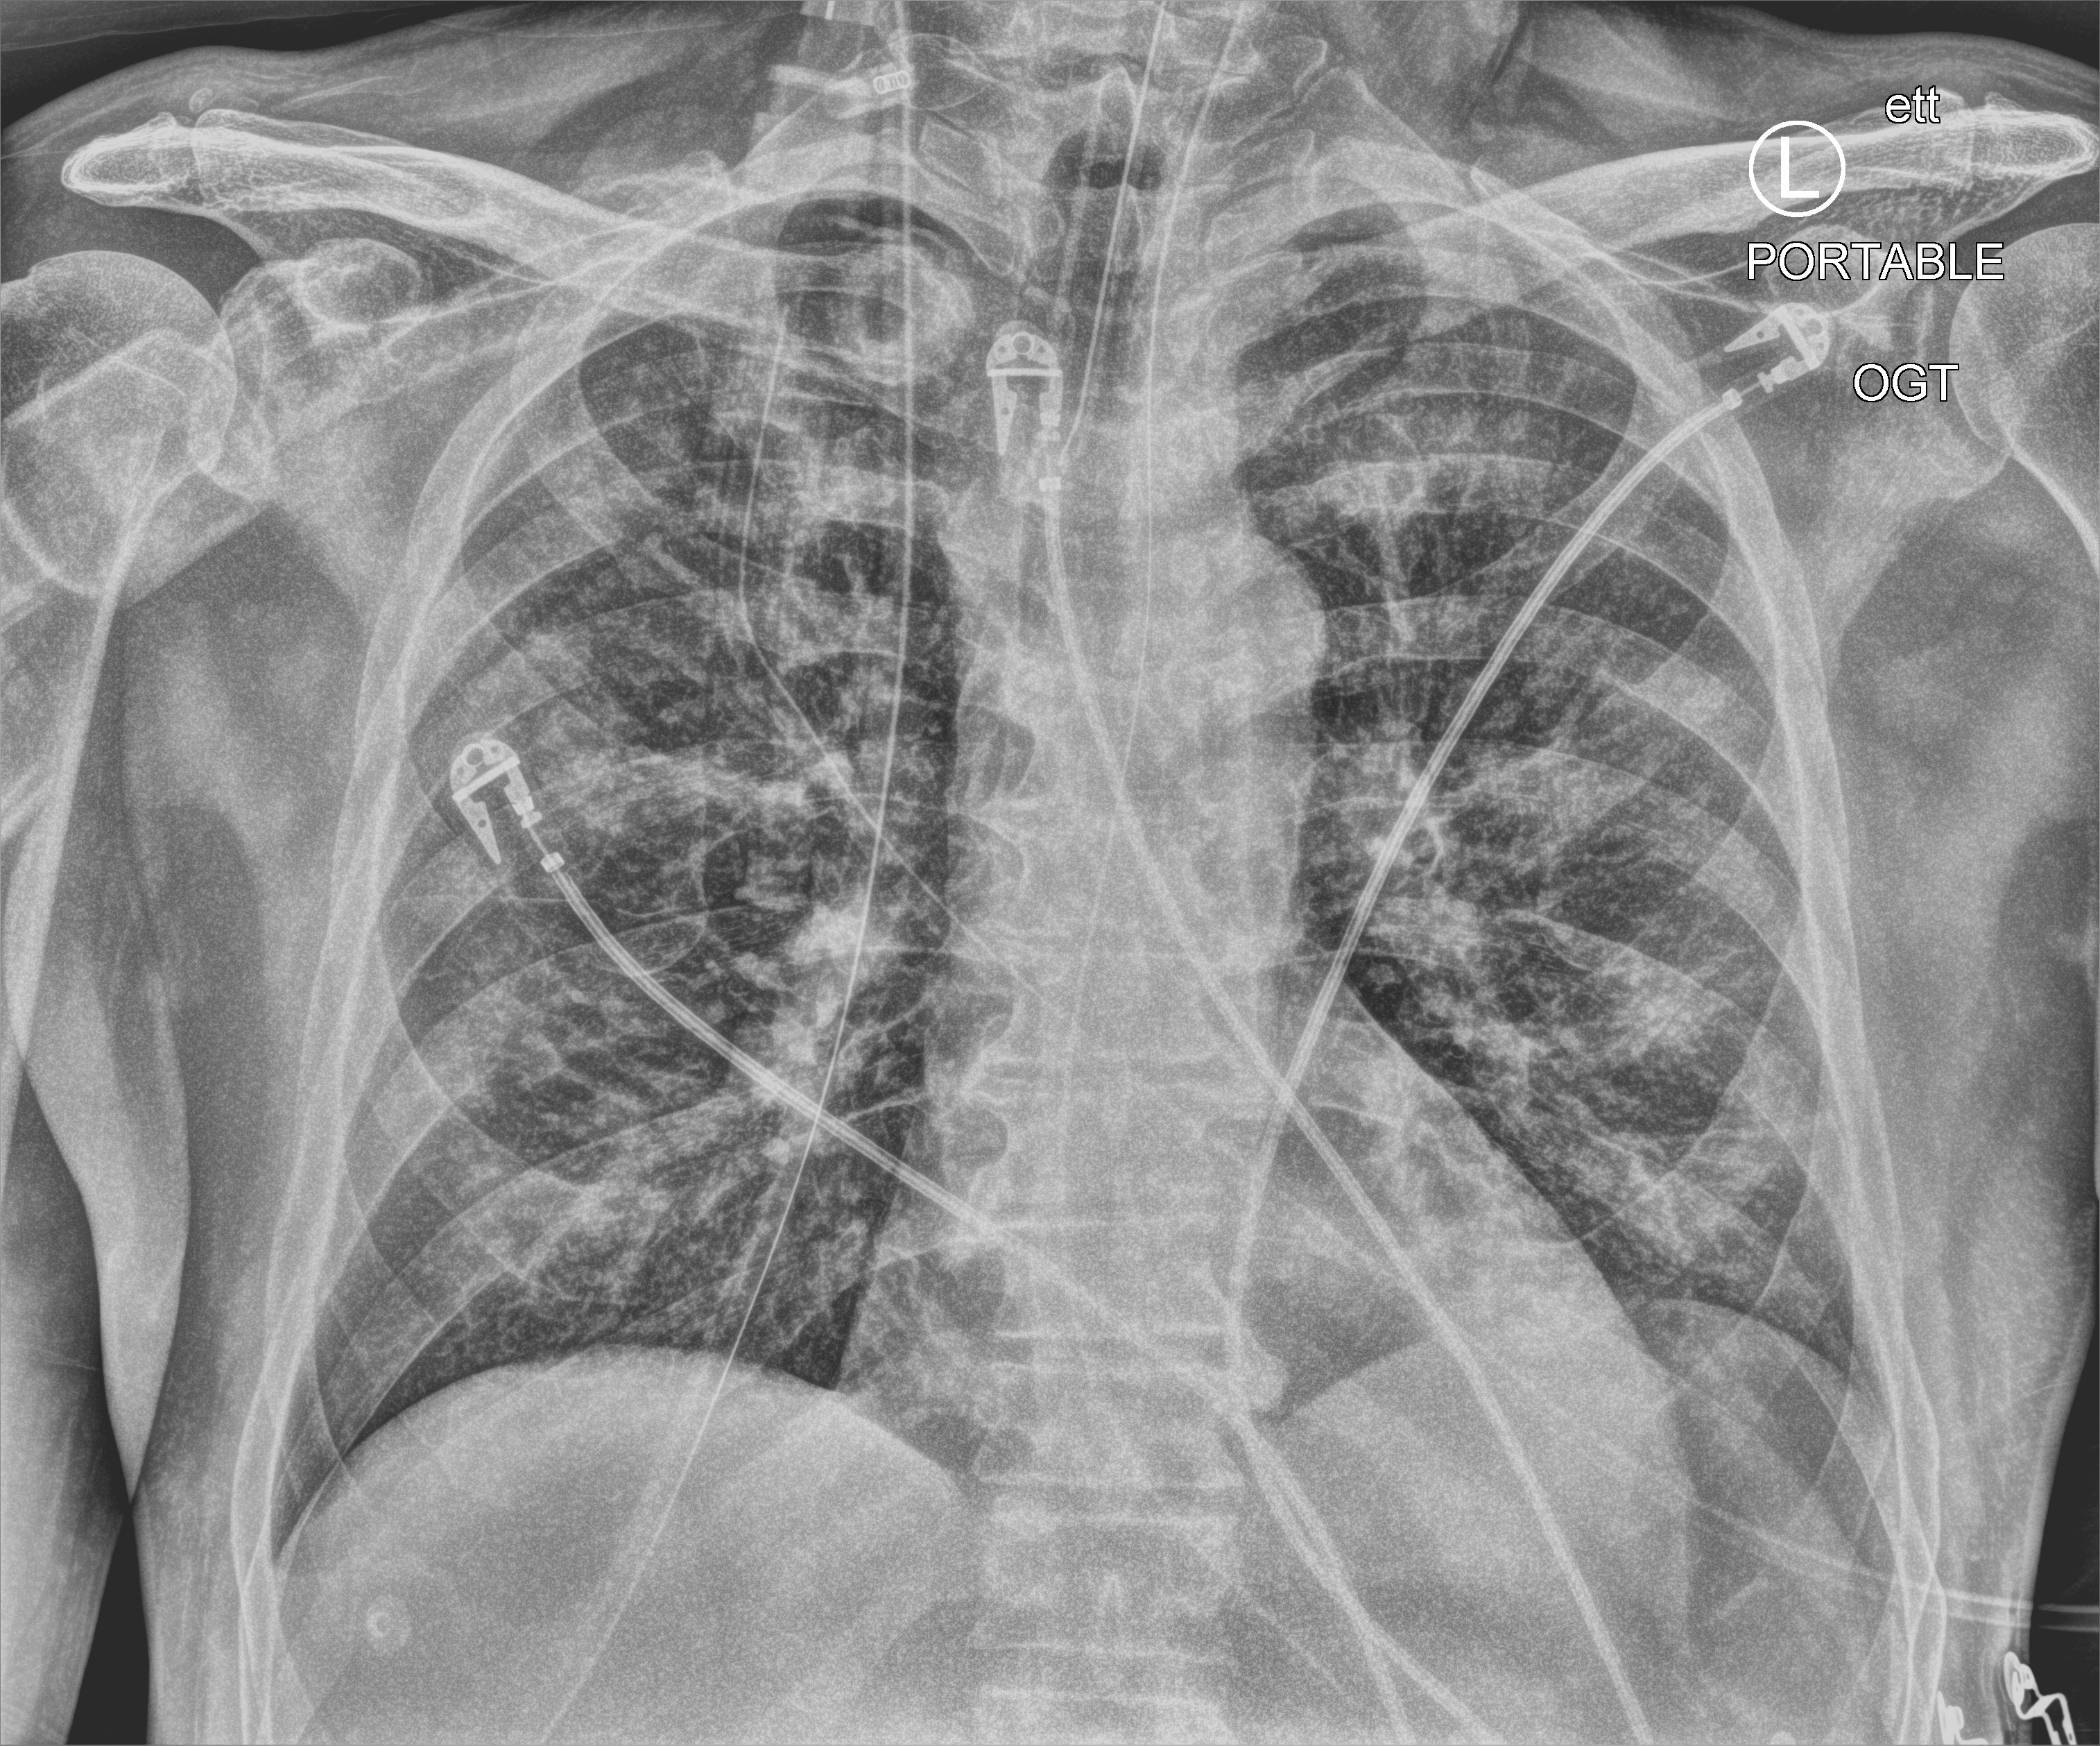
Portable chest radiograph; anteroposterior (AP) projection. Patient hospitalised with COVID-19; male, aged 60–74 years.
From the hospital-stay record, not from the radiograph (when in the stay this image was taken is not recorded): chronic kidney disease (admission record): no; mechanically ventilated during this hospital stay: yes; hypertension (admission record): yes.